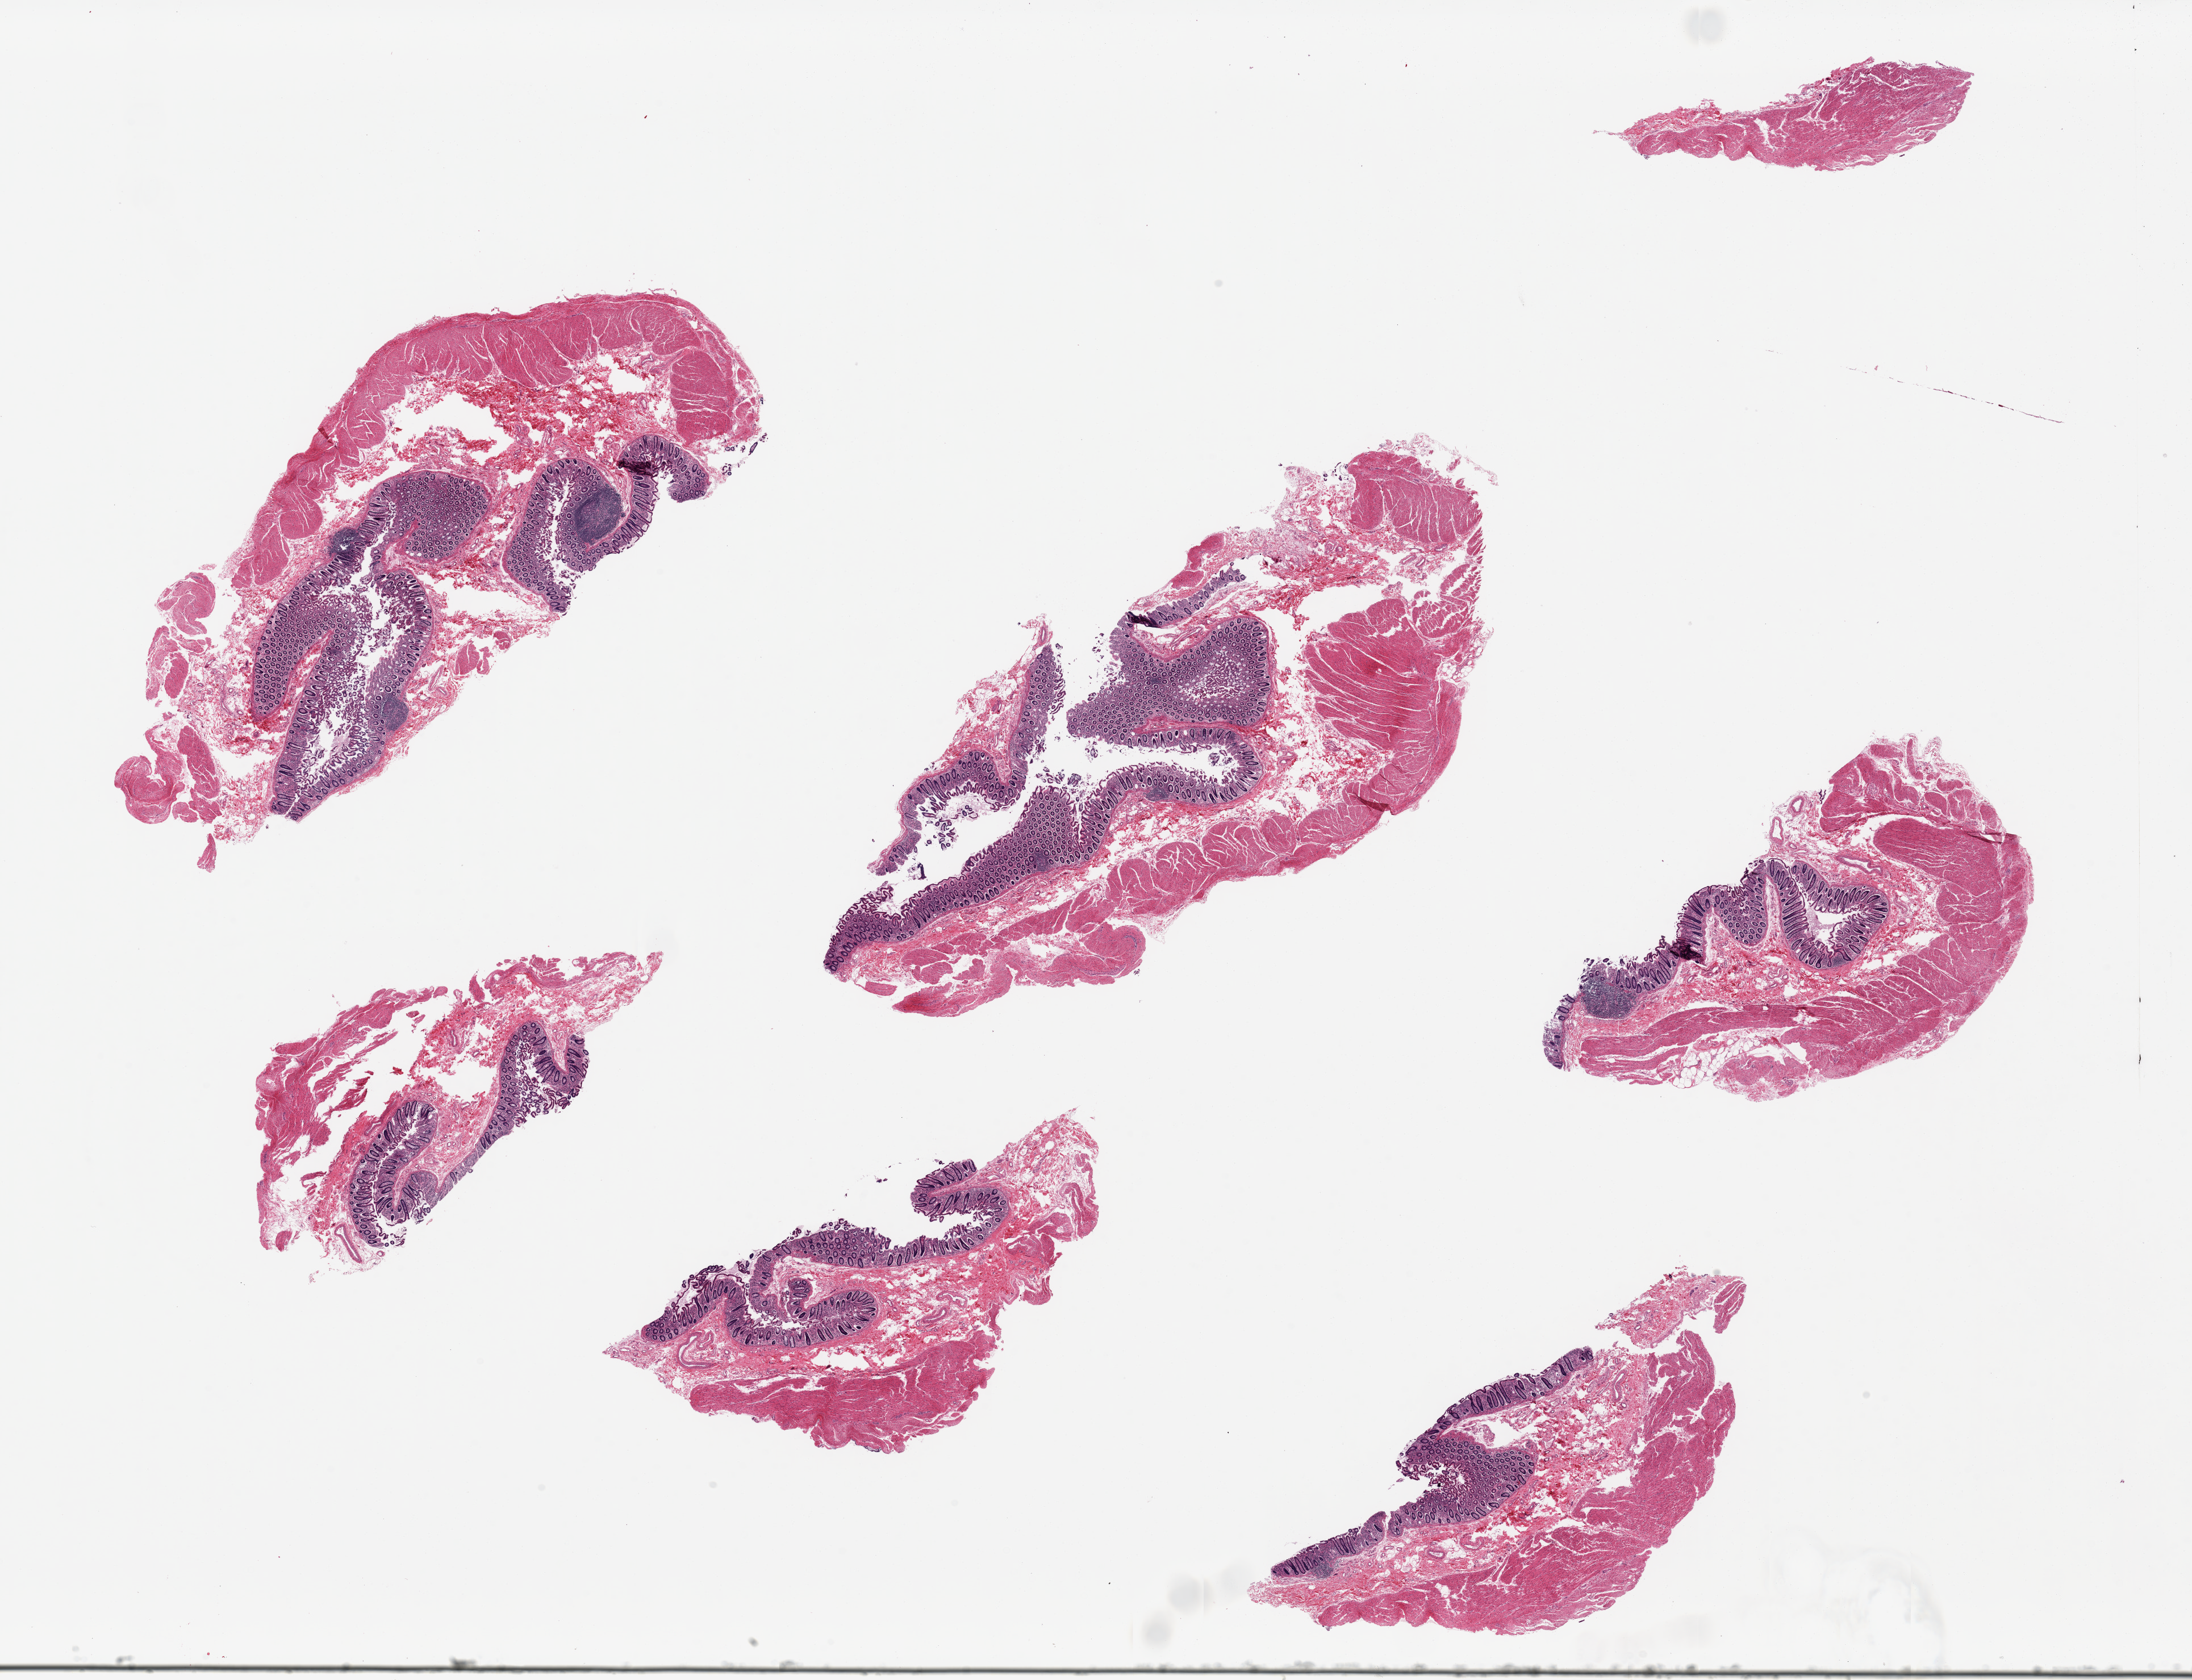
Whole-slide image, H&E stain, shown as a low-resolution overview of the whole scanned area (about 30.5 x 23.4 mm). PAXgene-fixed paraffin-embedded (PFPE) section. Sampled site (target tissue): transverse colon. Donor tissue sample. Male donor.
Review note (as recorded): 6 pieces, ~7x2.5mm. Mucosa reasonably well-preserved, ~25-30% of thickness.